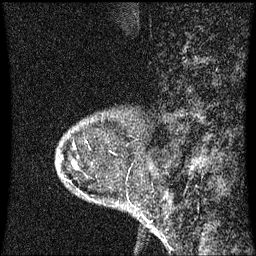
Breast MRI (dynamic contrast-enhanced), one sagittal slice; slice 12 of 60 in the series (ordered by position); dynamic contrast-enhanced series, image 2 of 3 at this slice position (ordered by acquisition); 1.5 T; TE 4.2 ms, TR 8.9 ms; 2 mm slice thickness; 256 × 256 image matrix, field of view 200 × 200 mm. Patient: female, 53 years. From the clinical record (not read from this slice): setting: breast cancer imaged before/during neoadjuvant chemotherapy; receptor status: HR-positive, HER2-negative.
Structures marked on this image (semi-automatic segmentation, software-assisted and operator-edited):
- analysis volume of interest (the breast-tissue region the enhancement analysis was run in; not a lesion): bounding box (x1, y1, x2, y2) in pixels: (62, 144, 89, 171)
- tumour enhancement mask (voxels above the 70 % enhancement threshold inside the analysis volume of interest): (74, 164, 77, 167)